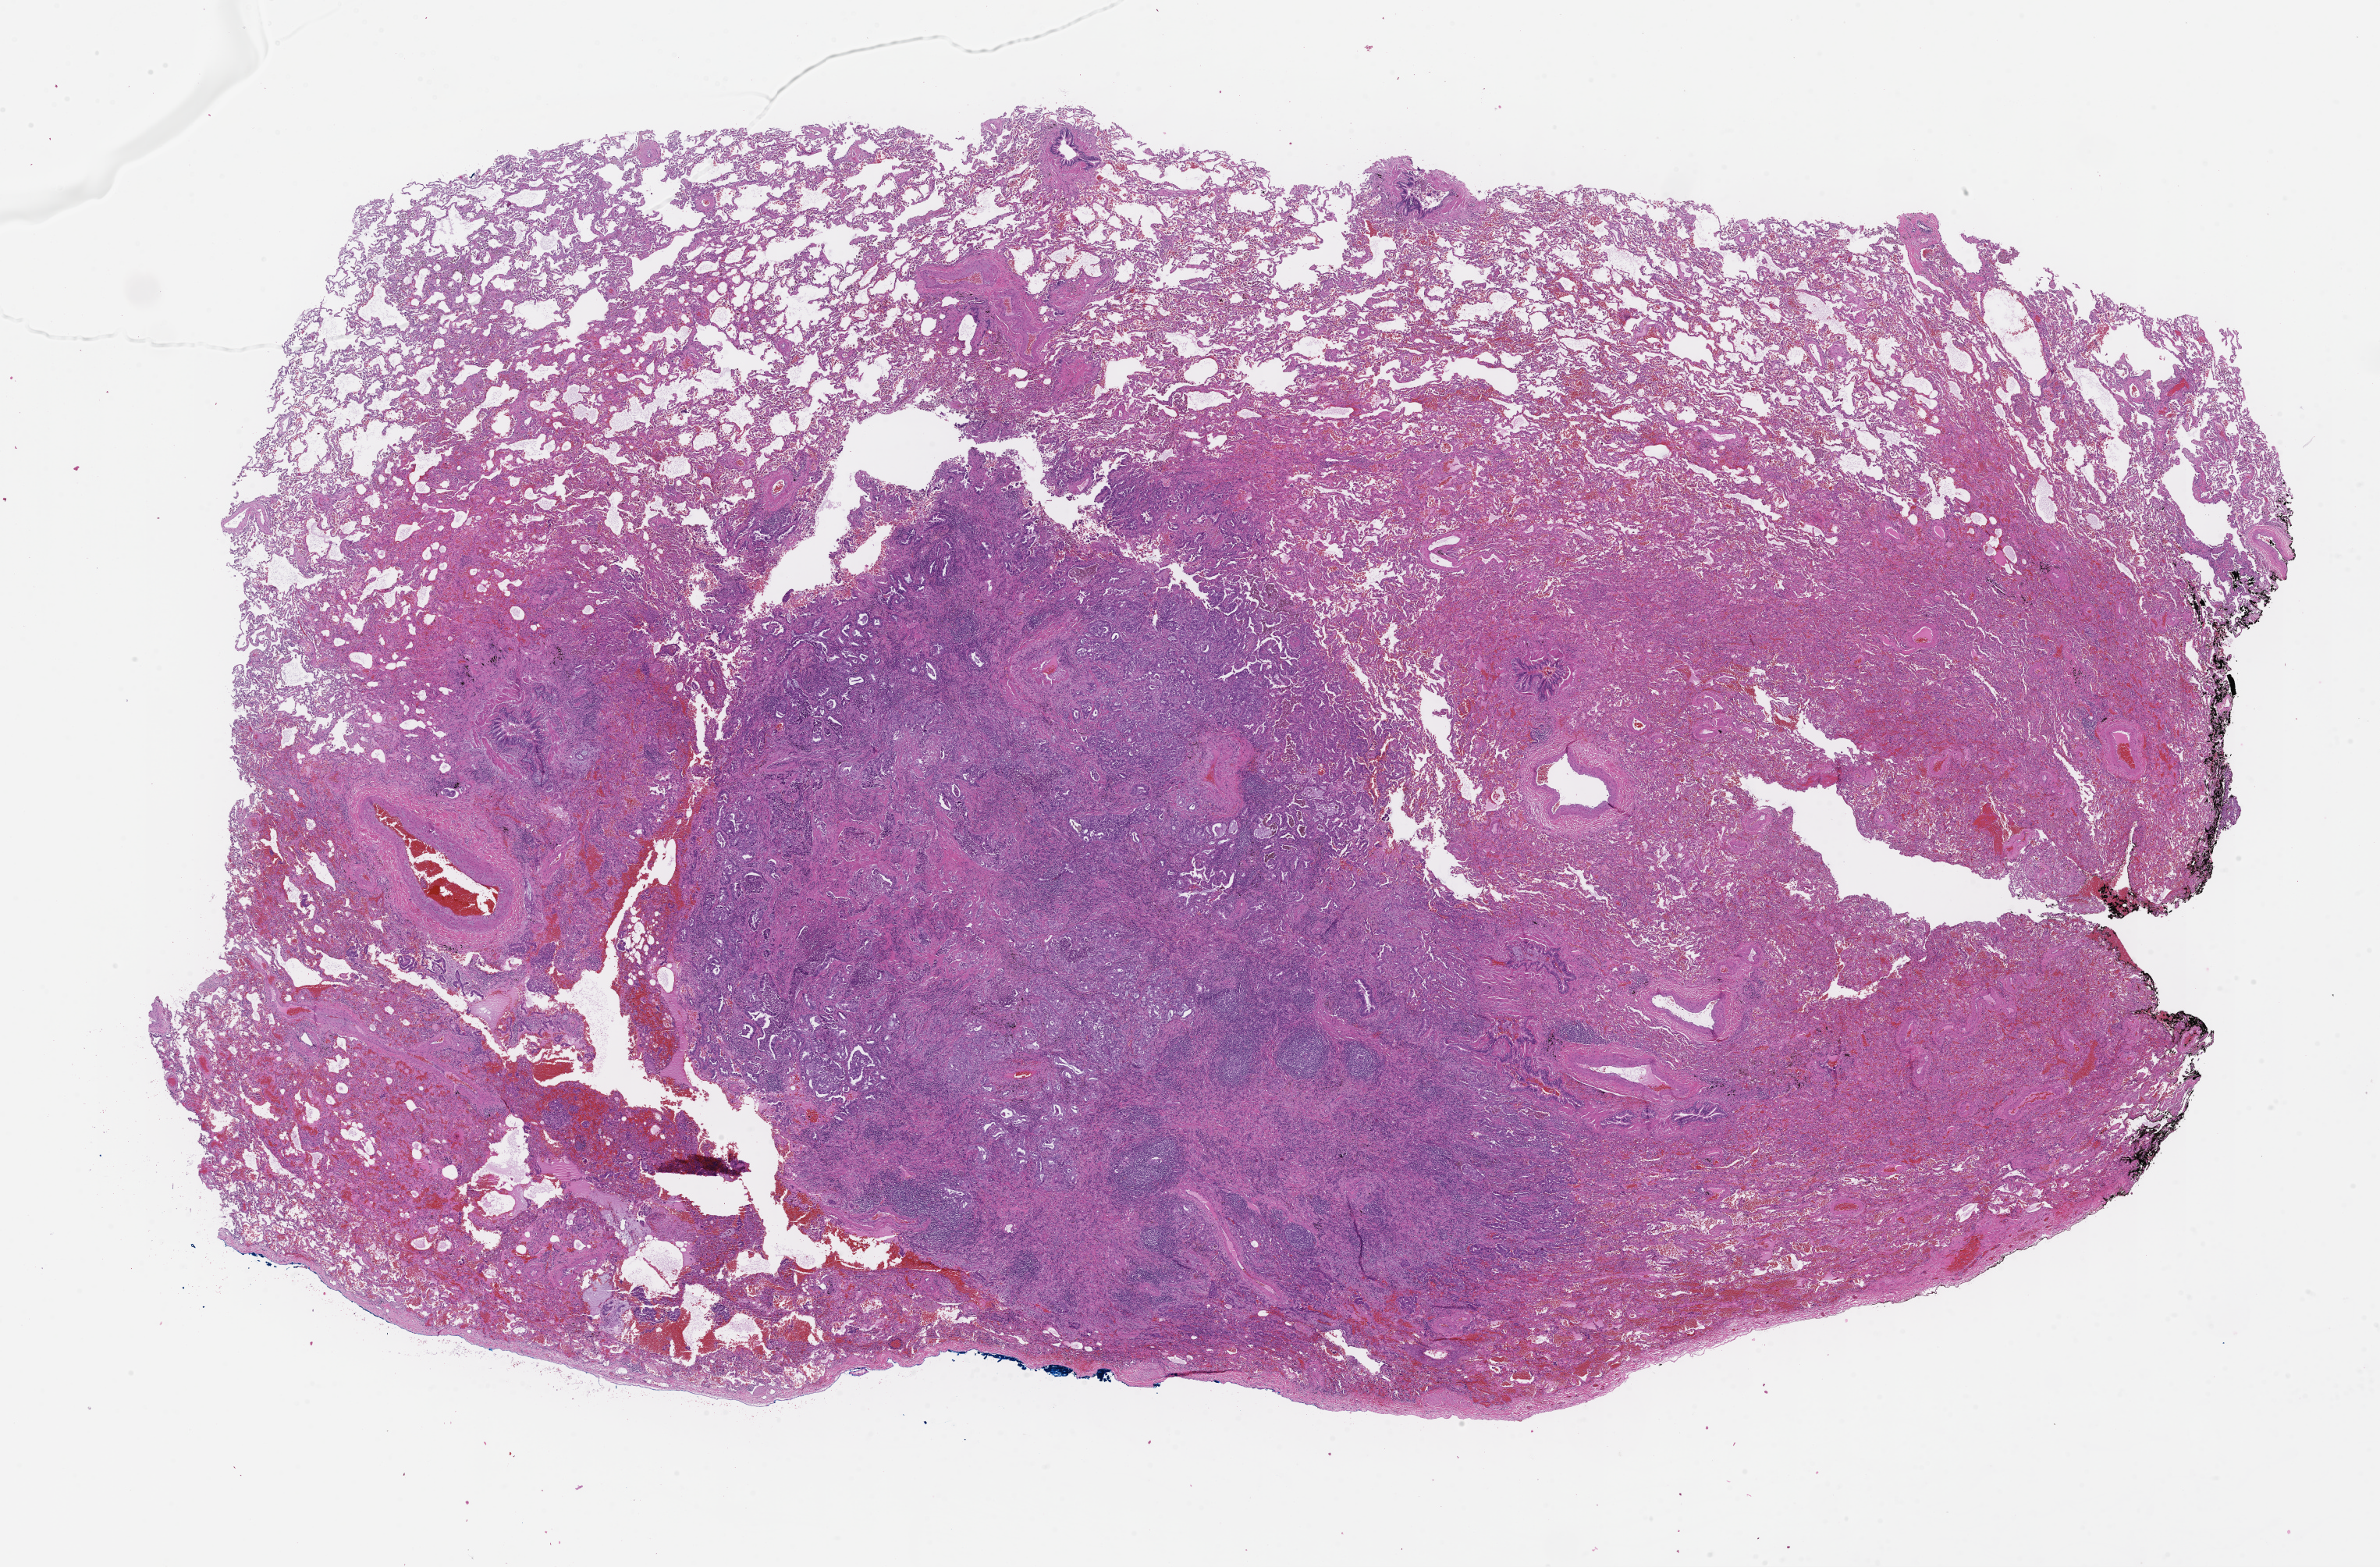
Digitized haematoxylin and eosin-stained section — shown as a low-resolution overview of the whole scanned area (about 24.6 x 16.2 mm). Formalin-fixed, paraffin-embedded (FFPE) tissue. Tissue site: lung. Specimen time point: collected at baseline (before treatment). Female patient.
- this section: primary tumor
- diagnosis: Non-Small Cell Lung Carcinoma